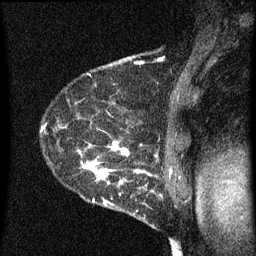
Breast MRI (dynamic contrast-enhanced), one sagittal slice. Position 49 of 60 along the scan axis. Dynamic contrast-enhanced series, image 2 of 3 at this slice position (ordered by acquisition). 1.5 T. TE 4.2 ms, TR 8 ms. 256 × 256 image matrix, field of view 180 × 180 mm. Female patient, age 54 years.
Outlined on this slice (semi-automatically segmented with operator editing):
- analysis volume of interest (the breast-tissue region the enhancement analysis was run in; not a lesion): bounding box (x1, y1, x2, y2) in pixels: (49, 138, 164, 209)
- tumour enhancement mask (voxels above the 70 % enhancement threshold inside the analysis volume of interest): (78, 140, 147, 207)